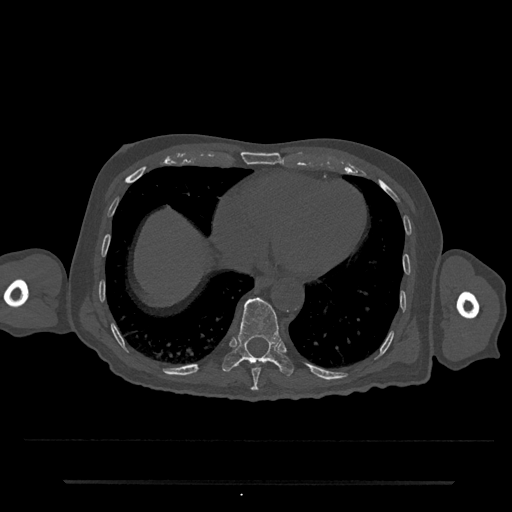
CT including the spine, one axial slice; position 326 of 797 along the scan axis; reconstruction kernel Br40s/3; 120 kVp; bone window (W 1800 / L 400 HU); 512 × 512 image matrix, field of view 427 × 427 mm. Patient: male, 74 years. Case-level facts recorded for this patient, not image findings: primary cancer: prostate.
Structures marked on this image (semi-automatic segmentation, software-assisted and operator-edited):
- T10 vertebra: bounding box [x1, y1, x2, y2] px = [222, 297, 294, 376]
- T9 vertebra: [251, 362, 262, 391]